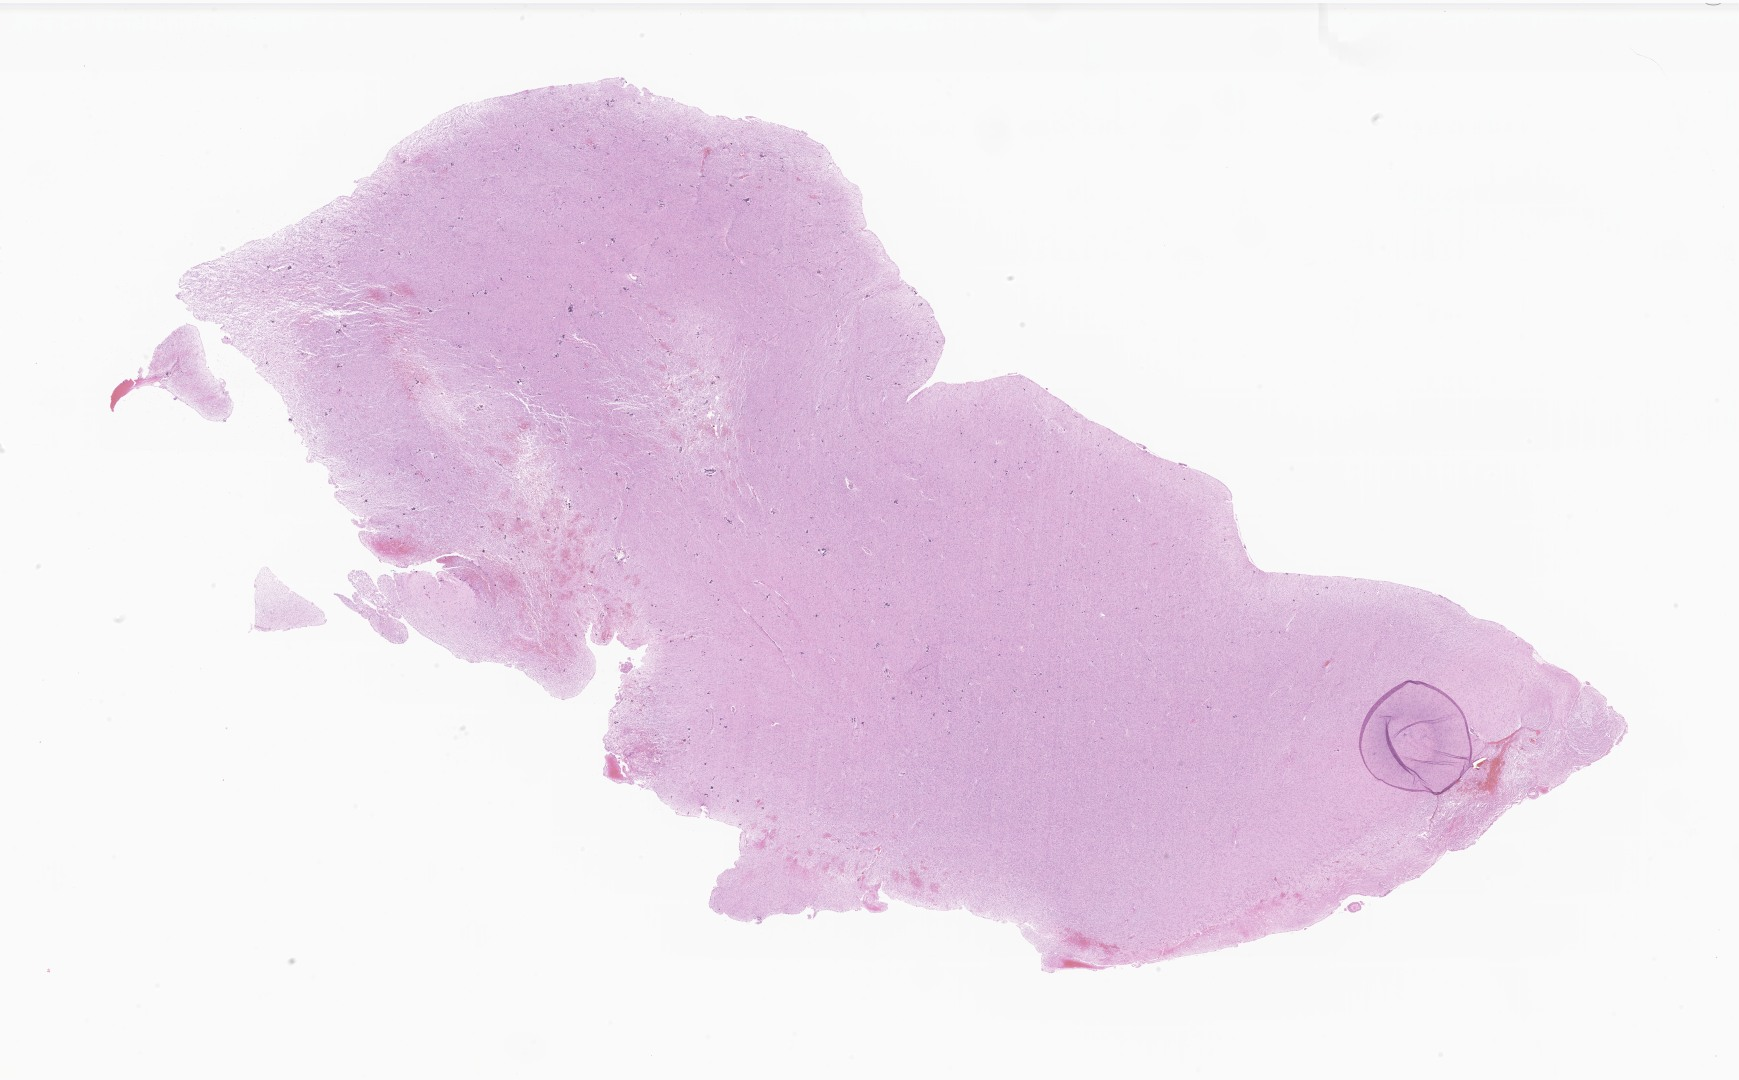
Whole-slide image, hematoxylin and eosin (H&E) stain of tumor tissue from the frontal lobe, whole scanned area (about 29.3 x 18.2 mm) shown as a low-resolution overview; FFPE section. Patient: female, age 355 days.
Recorded diagnosis: Glioma, malignant.